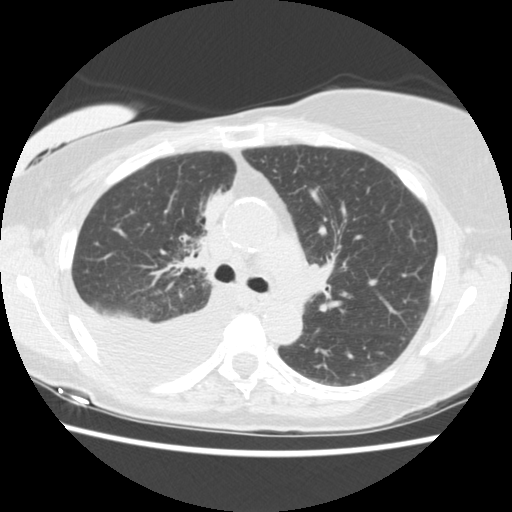
Low-dose screening chest CT, one axial slice. Slice 97 of 157 in the series (ordered by position). Lung window (W 1500 / L -600 HU). 2.5 mm slice thickness. 512 × 512 image matrix.
Structures marked on this image (expert manual segmentation):
- lesion 1 (tumor, upper lobe of right lung): bounding box (x1, y1, x2, y2) in pixels: (204, 190, 232, 228)